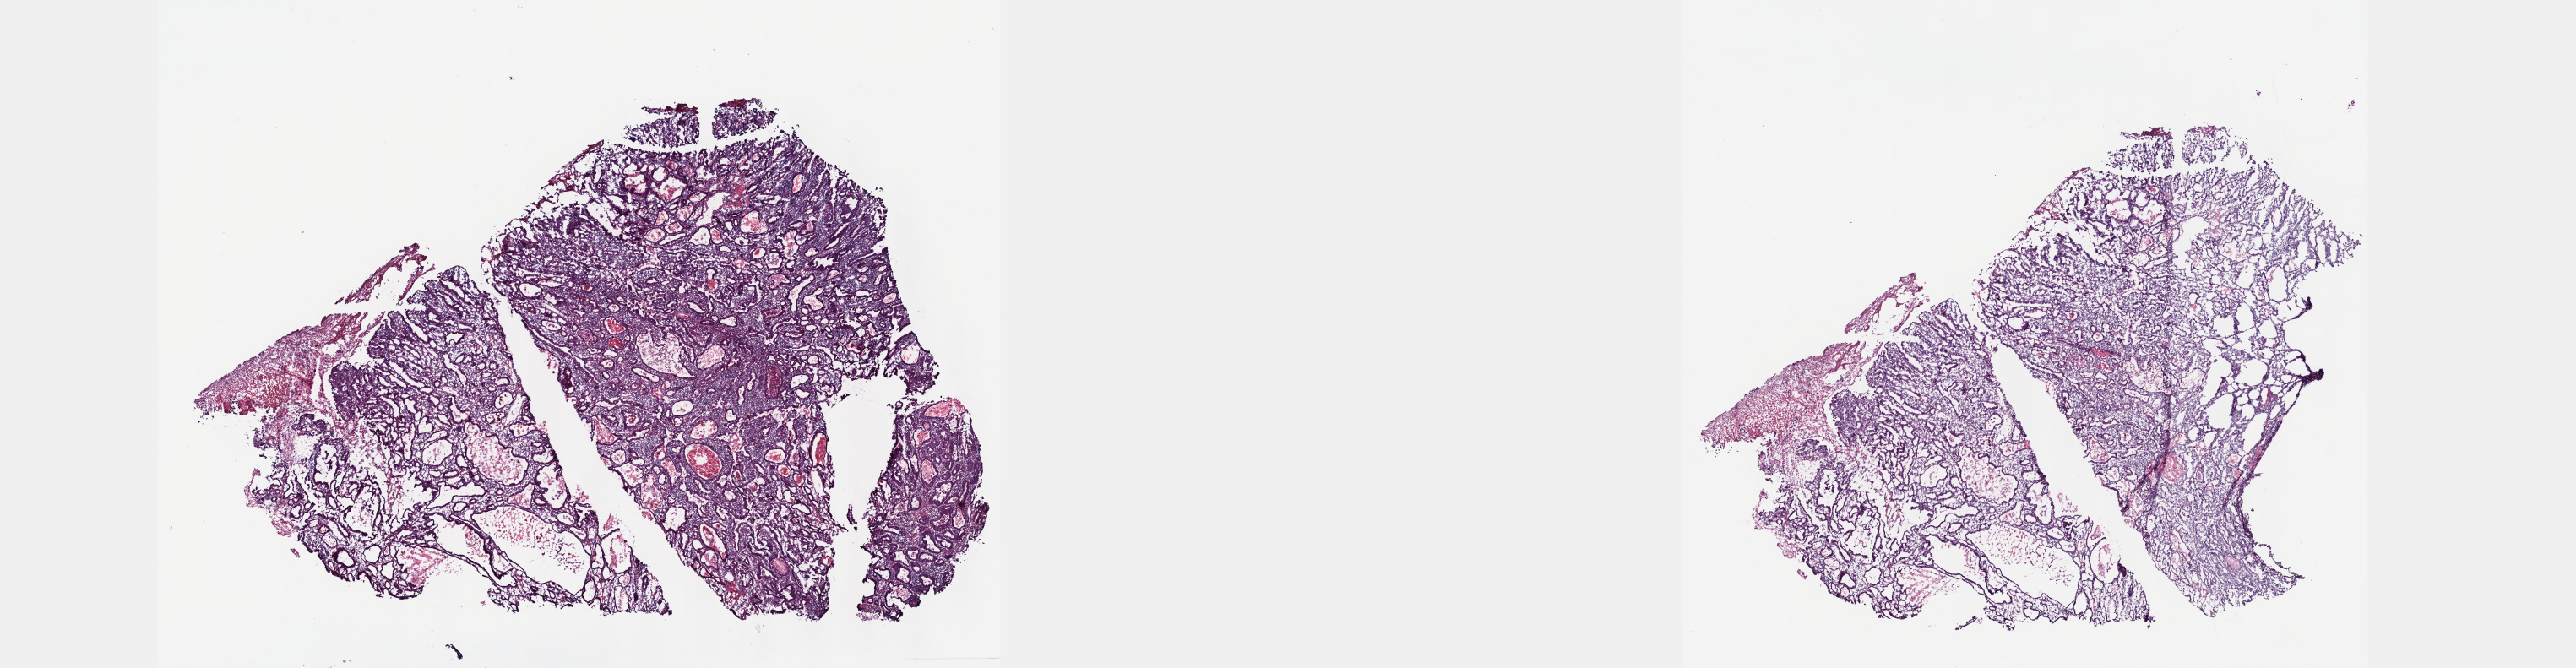
Whole-slide histology image, H&E-stained — low-resolution overview of the scanned area, about 24.6 x 6.4 mm (slide scanned at 40x); frozen section from the top of the tissue portion; esophagus, primary tumour sample. Male patient; age at initial diagnosis 68 years. Histologic grade: G2 (moderately differentiated). Pathologist review of this section (percent, as recorded): tumour cells 70%, tumour nuclei 70%, normal cells 0%, stromal cells 20%, necrosis 10%. Infiltration values recorded for this section: lymphocyte infiltration 40%, monocyte infiltration 20%, neutrophil infiltration 20%.
AJCC pathologic stage: III (5th edition). Lymph nodes positive (case pathology): 4 of 8 examined. Pathologic diagnosis: Adenocarcinoma, NOS (lower third of esophagus).